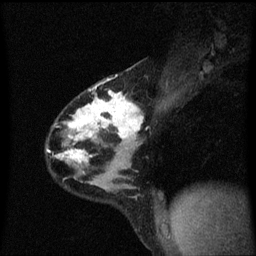
Breast MRI (dynamic contrast-enhanced), one sagittal slice. Slice 39 of 60 in the series (ordered by position). Dynamic contrast-enhanced series, image 2 of 3 at this slice position (ordered by acquisition). 1.5 T. TE 4.2 ms, TR 8.4 ms. 2 mm slice thickness. 256 × 256 image matrix, field of view 200 × 200 mm. Patient: female, 32 years.
Outlined on this slice (semi-automatically segmented with operator editing):
- analysis volume of interest (the breast-tissue region the enhancement analysis was run in; not a lesion): bounding box [x1, y1, x2, y2] px = [46, 76, 149, 169]
- tumour enhancement mask (voxels above the 70 % enhancement threshold inside the analysis volume of interest): [48, 78, 144, 163]